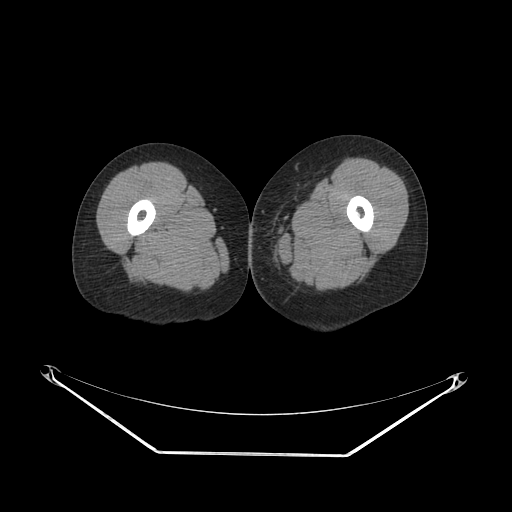
CT of an extremity soft-tissue mass (from a PET/CT study), one axial slice. Position 33 of 267 along the scan axis. Reconstruction kernel SOFT. Soft-tissue window (W 400 / L 40 HU). 512 × 512 image matrix, field of view 500 × 500 mm. Female patient. Case-level facts recorded for this patient, not image findings: histological type: leiomyosarcoma; grade: high; site of the primary tumour: groin.
Annotated regions visible in this slice (expert contour drawn on MRI and transferred to this co-registered scan by the dataset authors):
- gross tumour volume including surrounding oedema: bounding box <249,230,277,247> (left, top, right, bottom; pixels)